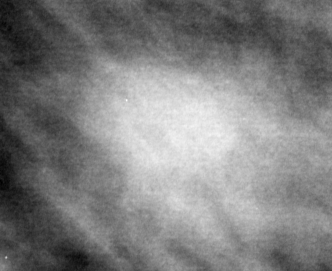
Region of interest cut from a scanned film mammogram (one marked finding), right breast, MLO view, BI-RADS breast density category 2 (scale 1–4).
Mass, shape irregular, margins ill defined; BI-RADS assessment category 4; pathology result (as recorded, not read from the image): malignant.